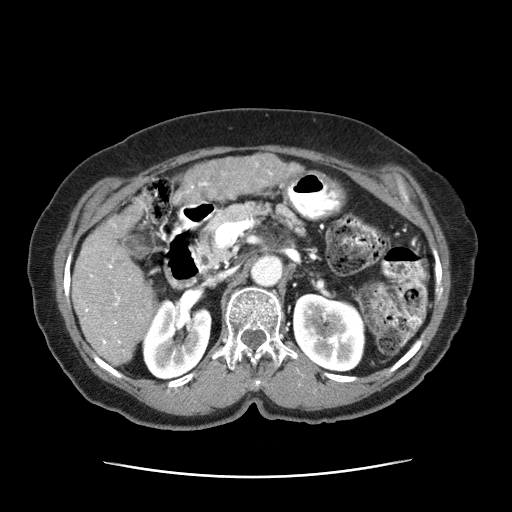
Contrast-enhanced abdominal CT (liver protocol), one axial slice; position 21 of 63 along the scan axis; reconstruction kernel STANDARD; 120 kVp; intravenous contrast given; soft-tissue window (W 400 / L 40 HU); 2.5 mm slice thickness; 512 × 512 image matrix, field of view 360 × 360 mm. Patient: female, 79 years. From the clinical record (not read from this slice): diagnosis: hepatocellular carcinoma (patient treated with transarterial chemoembolisation; whether this scan precedes or follows treatment is not stated here); TNM stage (as recorded): Stage-II.
Structures marked on this image (semi-automatic segmentation, software-assisted and operator-edited):
- abdominal aorta: bounding box <251,251,283,285> (left, top, right, bottom; pixels)
- liver parenchyma outside the tumour (the mass and vessels are separate outlines, so this box may not span the whole liver): <70,203,156,368>
- mass: <178,154,294,200>
- liver vessels: <85,264,131,345>